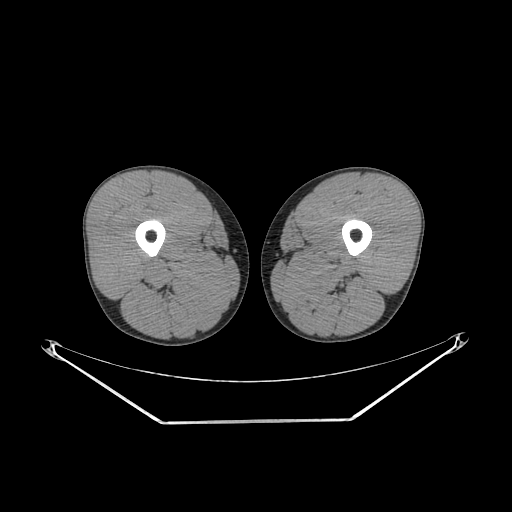
CT of an extremity soft-tissue mass (from a PET/CT study), one axial slice; reconstruction kernel SOFT; 140 kVp; soft-tissue window (W 400 / L 40 HU); 3.75 mm slice thickness; 512 × 512 image matrix. Male patient. From the clinical record (not read from this slice): histological type: extraskeletal osteosarcoma; grade: high; site of the primary tumour: left adductur.
Annotated regions visible in this slice (expert contour drawn on MRI and transferred to this co-registered scan by the dataset authors):
- gross tumour volume (mass): bounding box <283,249,364,286> (left, top, right, bottom; pixels)